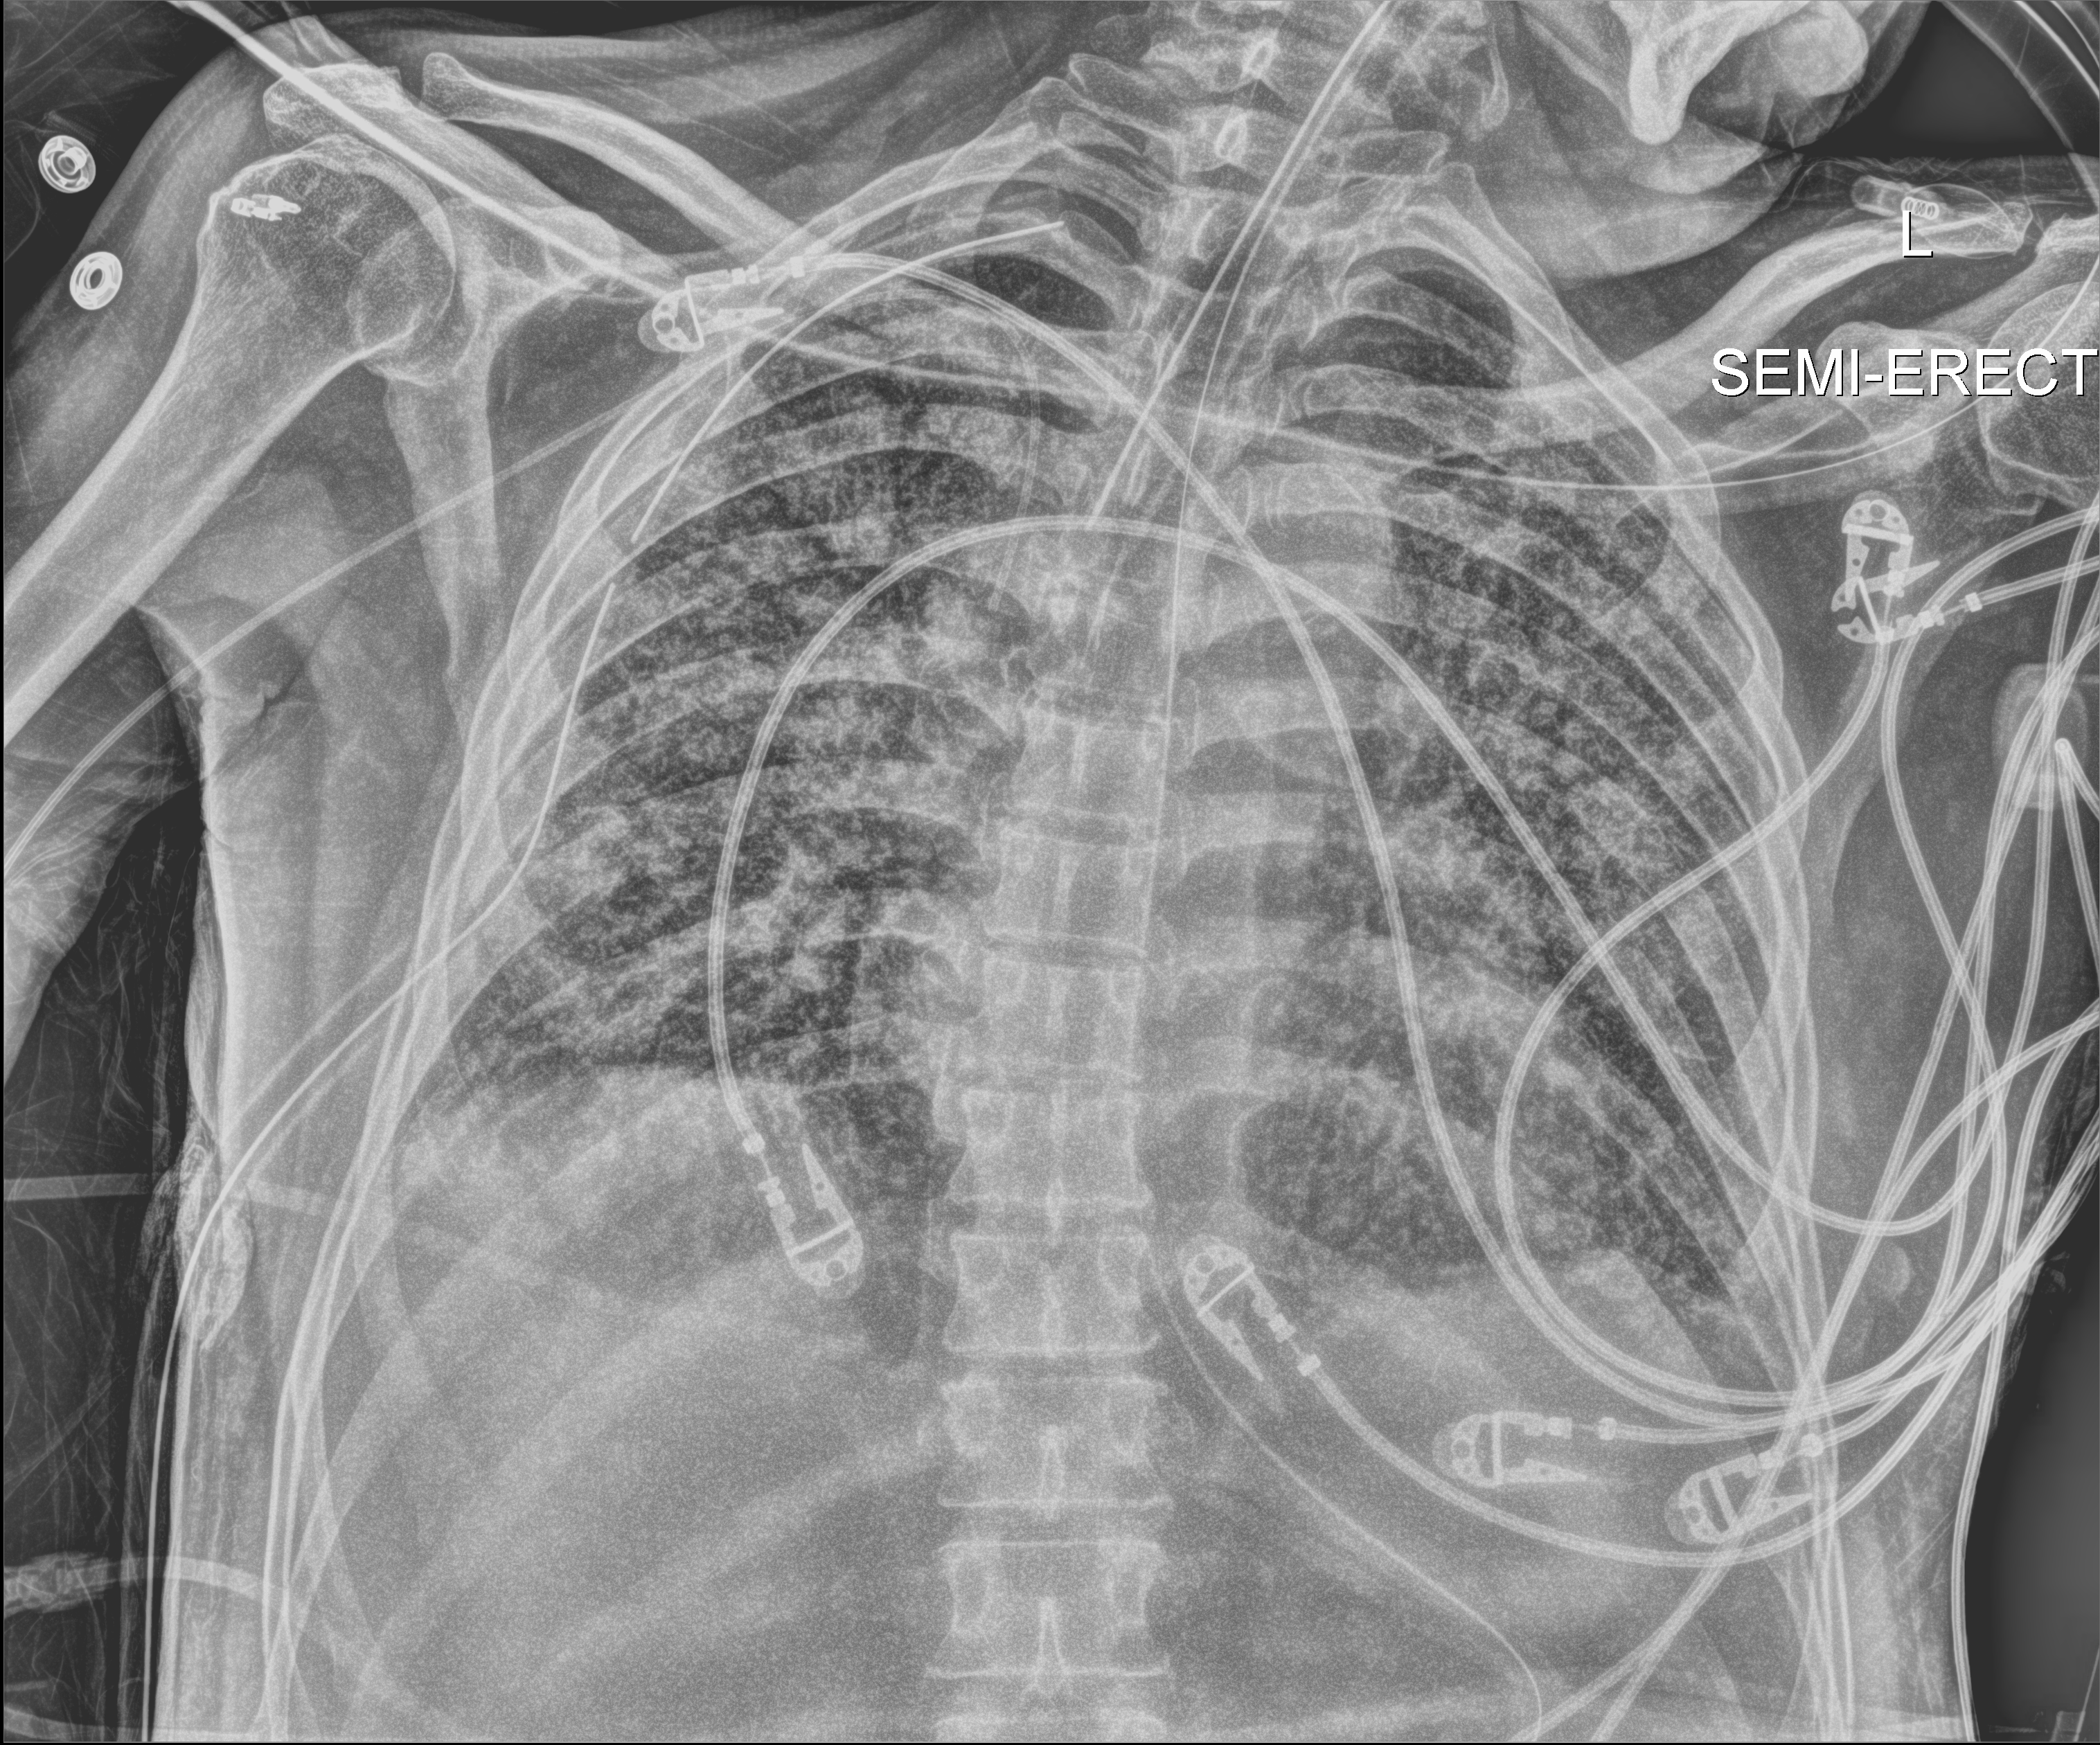
Chest X-ray (portable), anteroposterior (AP) projection. Patient hospitalised with COVID-19; male, aged 60–74 years.
Admission-level facts for this patient (not findings on this image; timing relative to this image not recorded):
- mechanically ventilated during this hospital stay: yes
- diabetes (admission record): no